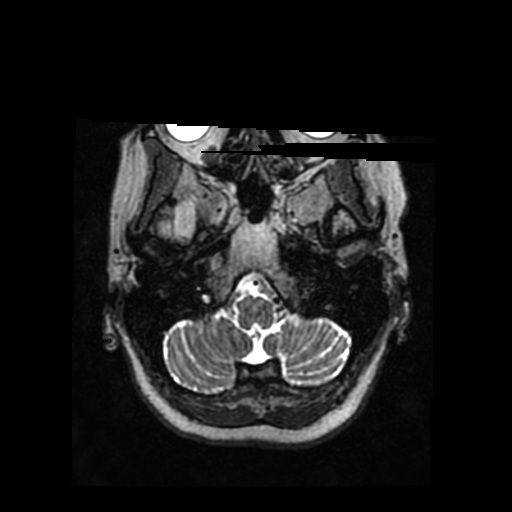
Brain MRI from a brain-tumour surgery series, one axial slice. Position 192 of 290 along the scan axis. 0.83 mm slice thickness. 512 × 512 image matrix, field of view 240 × 240 mm. Case-level facts recorded for this patient, not image findings: histopathology: Glioblastoma; WHO grade: 4; IDH mutation: no.
Annotated regions visible in this slice (manually delineated by an expert):
- tumour: box from (x=191, y=201) to (x=204, y=222) px